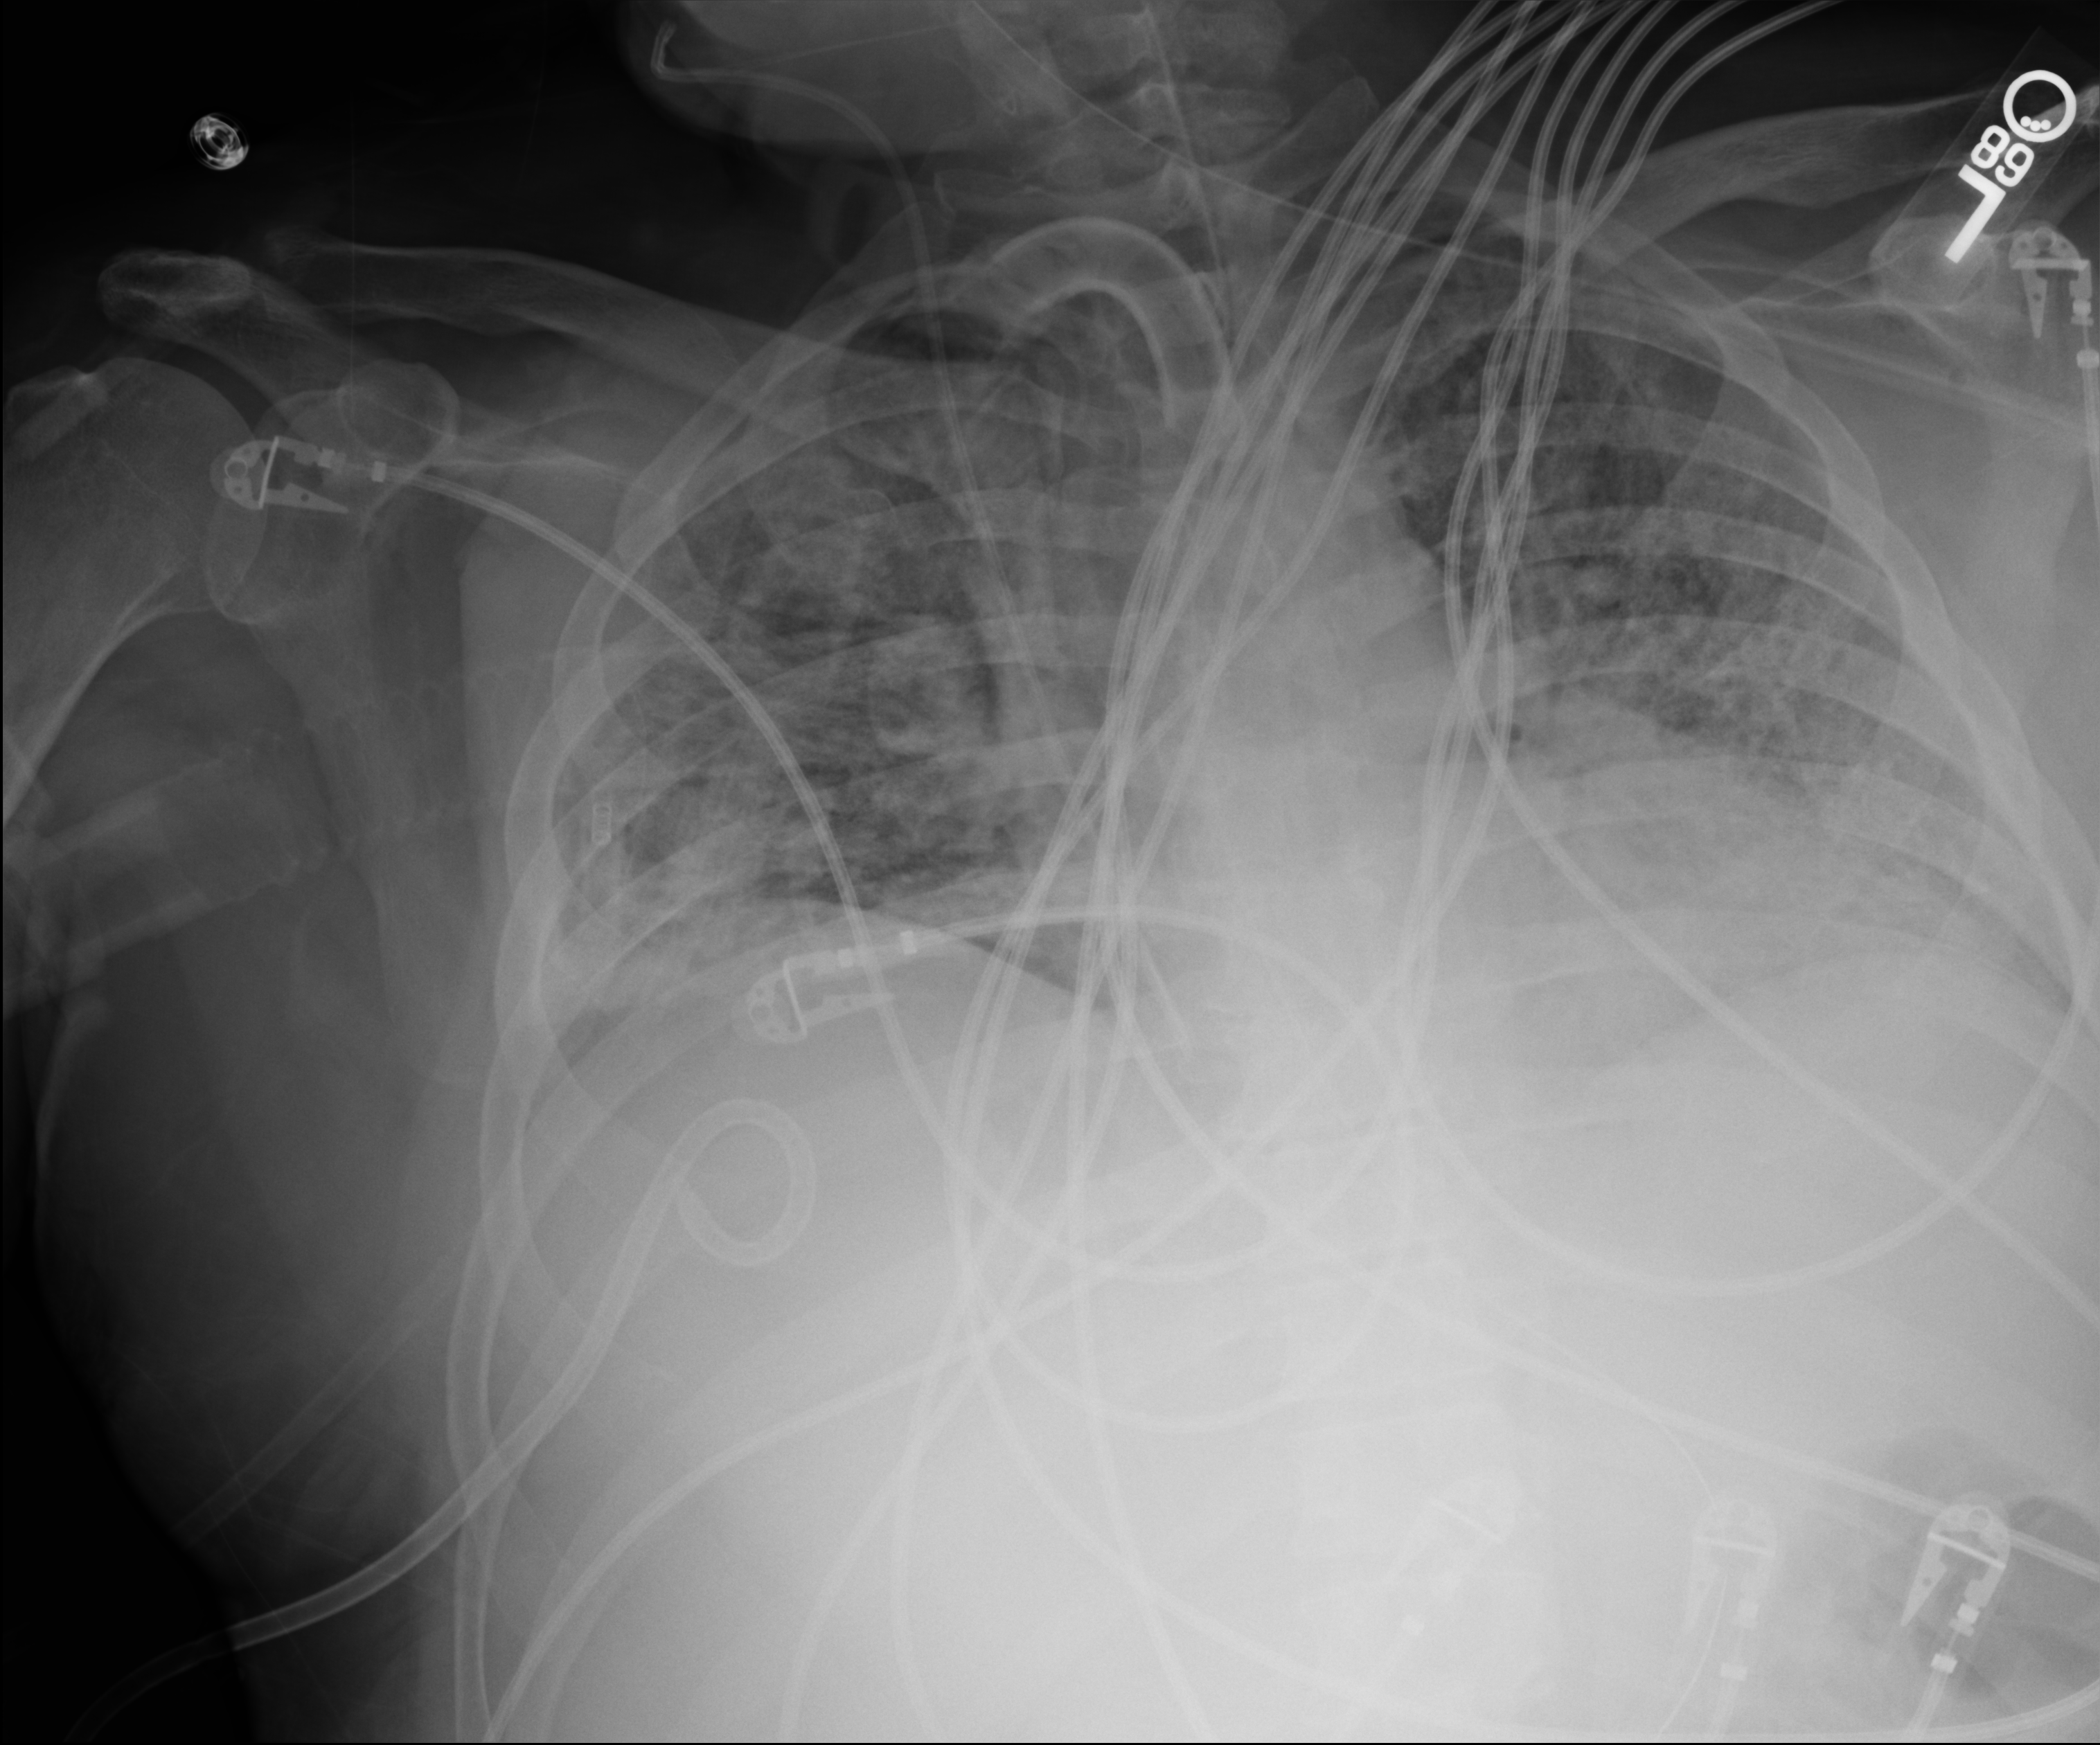
Chest X-ray (portable); anteroposterior (AP) projection. Male patient hospitalised with COVID-19, age 18–59 years.
Admission-level facts for this patient (not findings on this image; timing relative to this image not recorded): mechanically ventilated during this hospital stay: yes; admitted to intensive care during this hospital stay: yes.